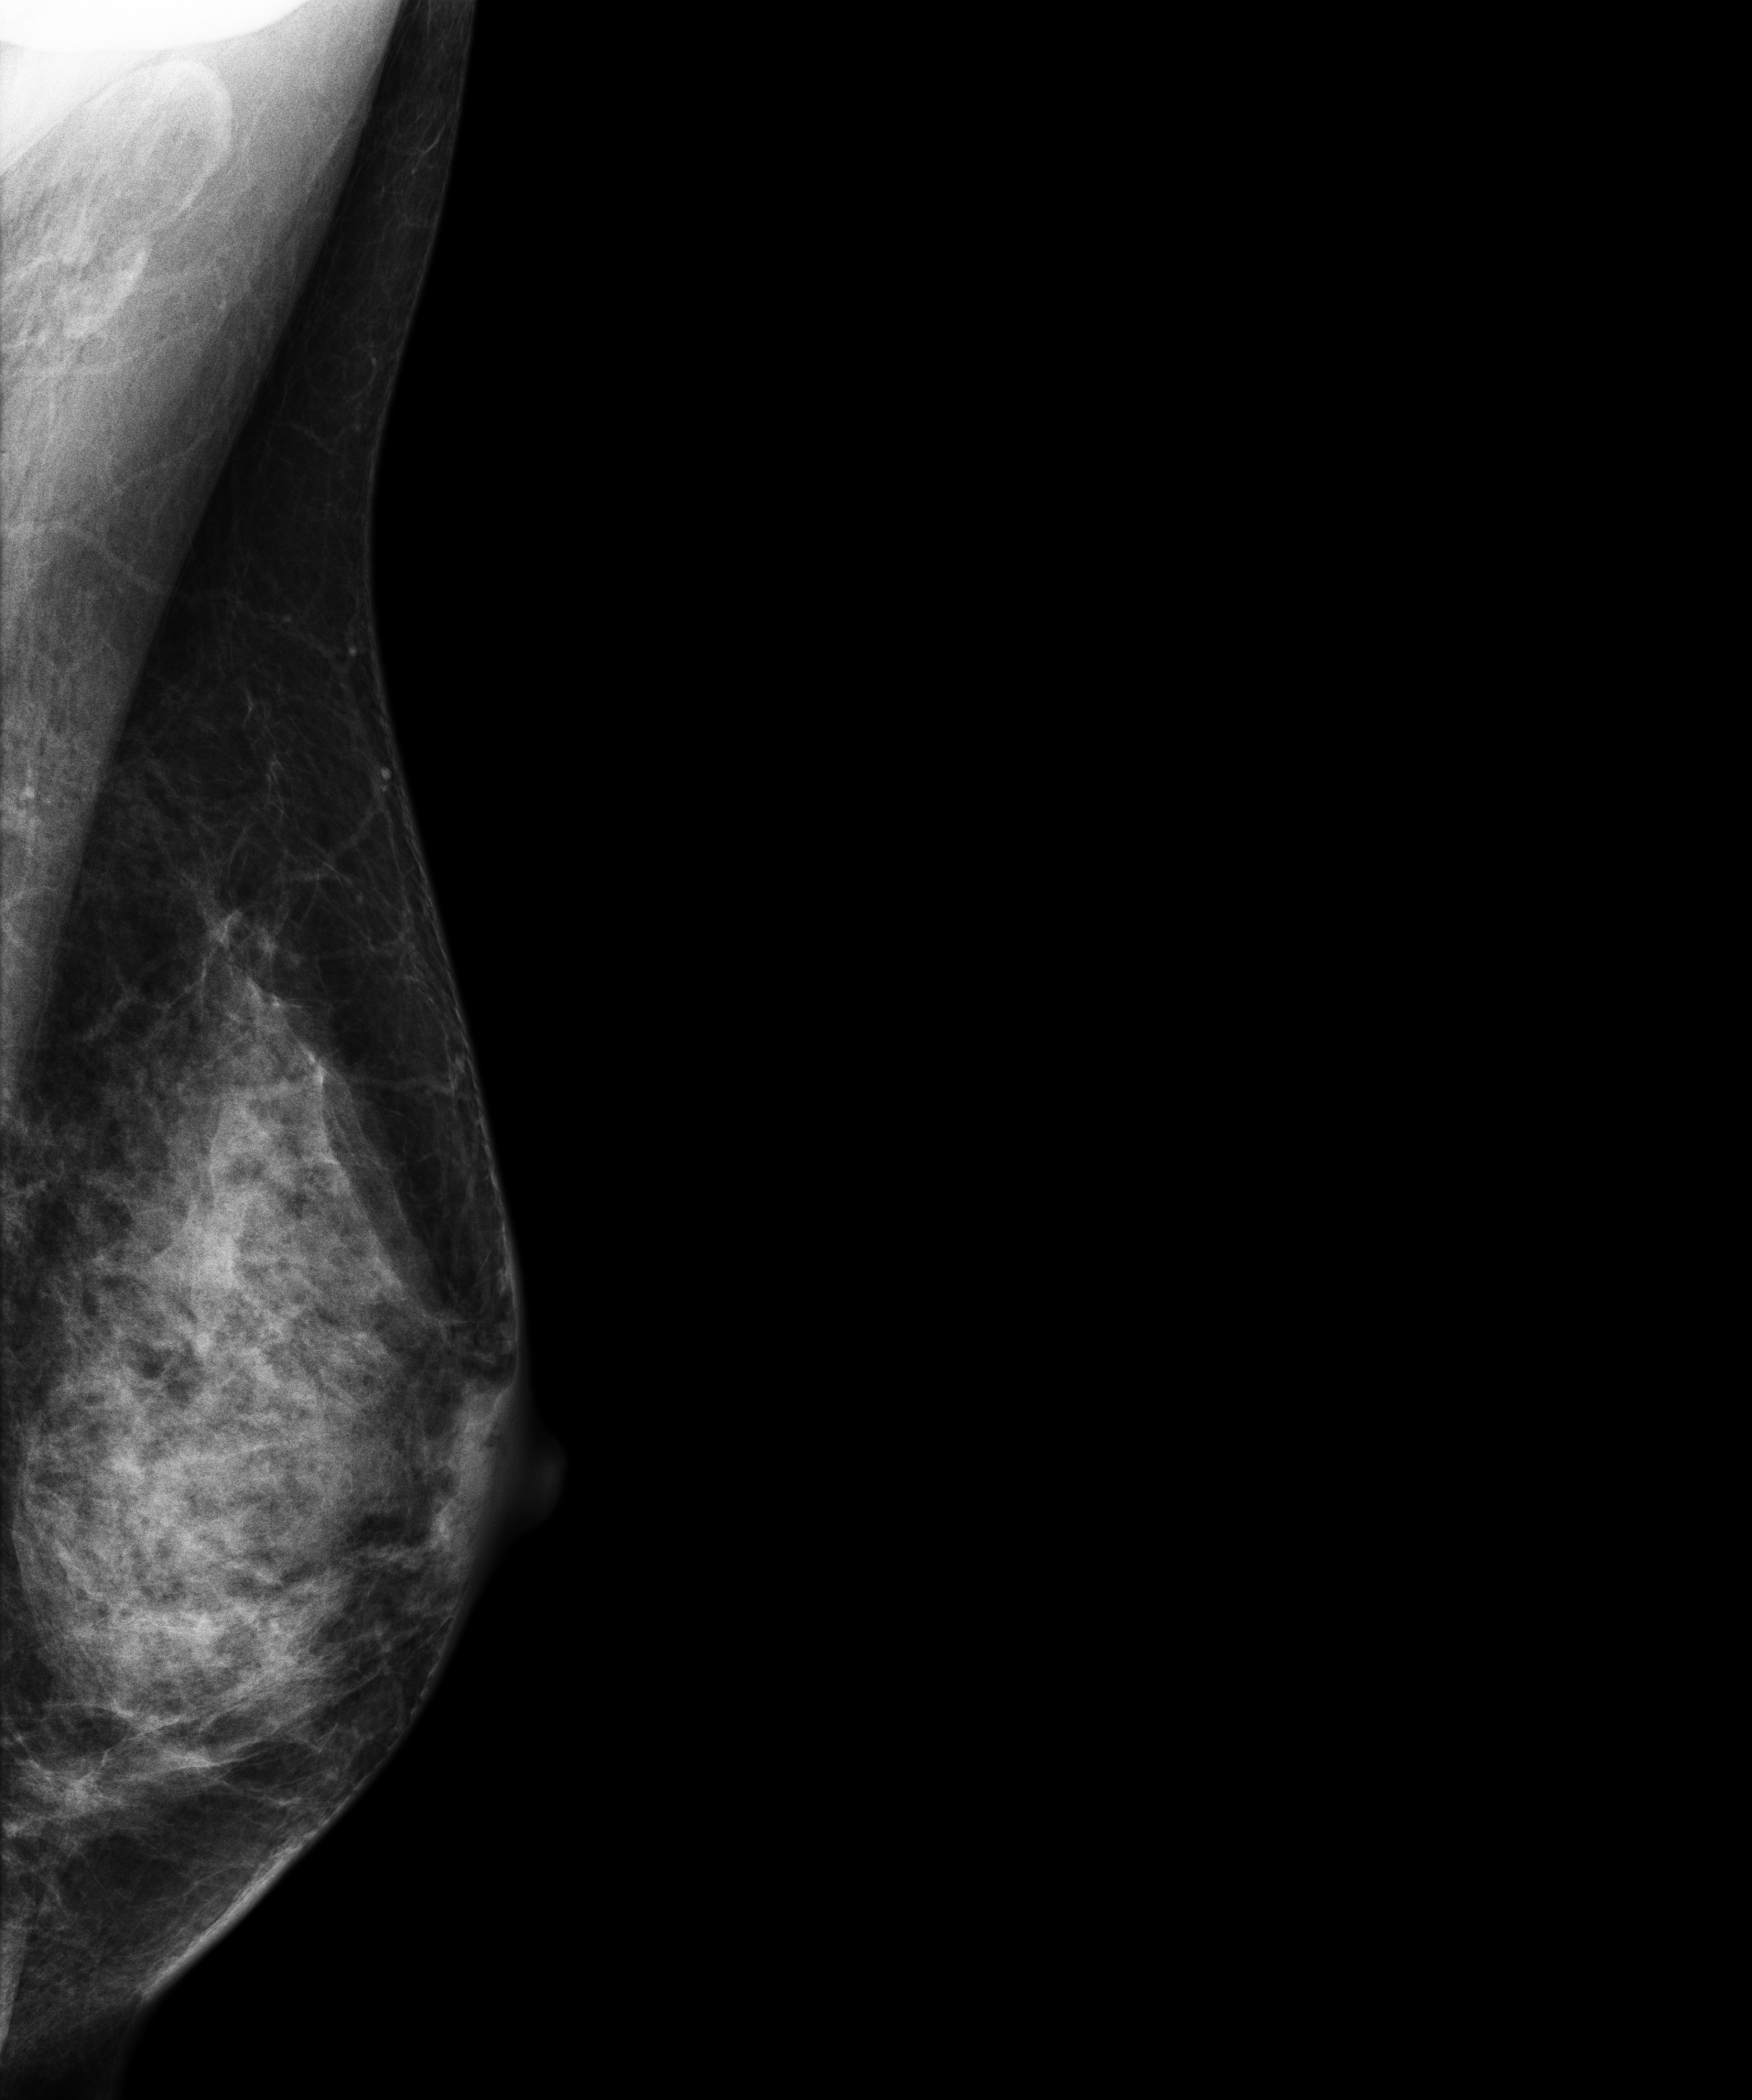
Digital mammogram (FFDM), left breast, mediolateral oblique (MLO) view, screening examination, compressed breast thickness 52 mm, system: Senographe Essential ADS_56.21.3. Female patient, age 55 years.
- BI-RADS breast density category at the screening exam (both breasts, scale 1–4): 4
- final BI-RADS assessment for this screening round (tomosynthesis exam, both breasts): category 1
- recall: no recall after this screen